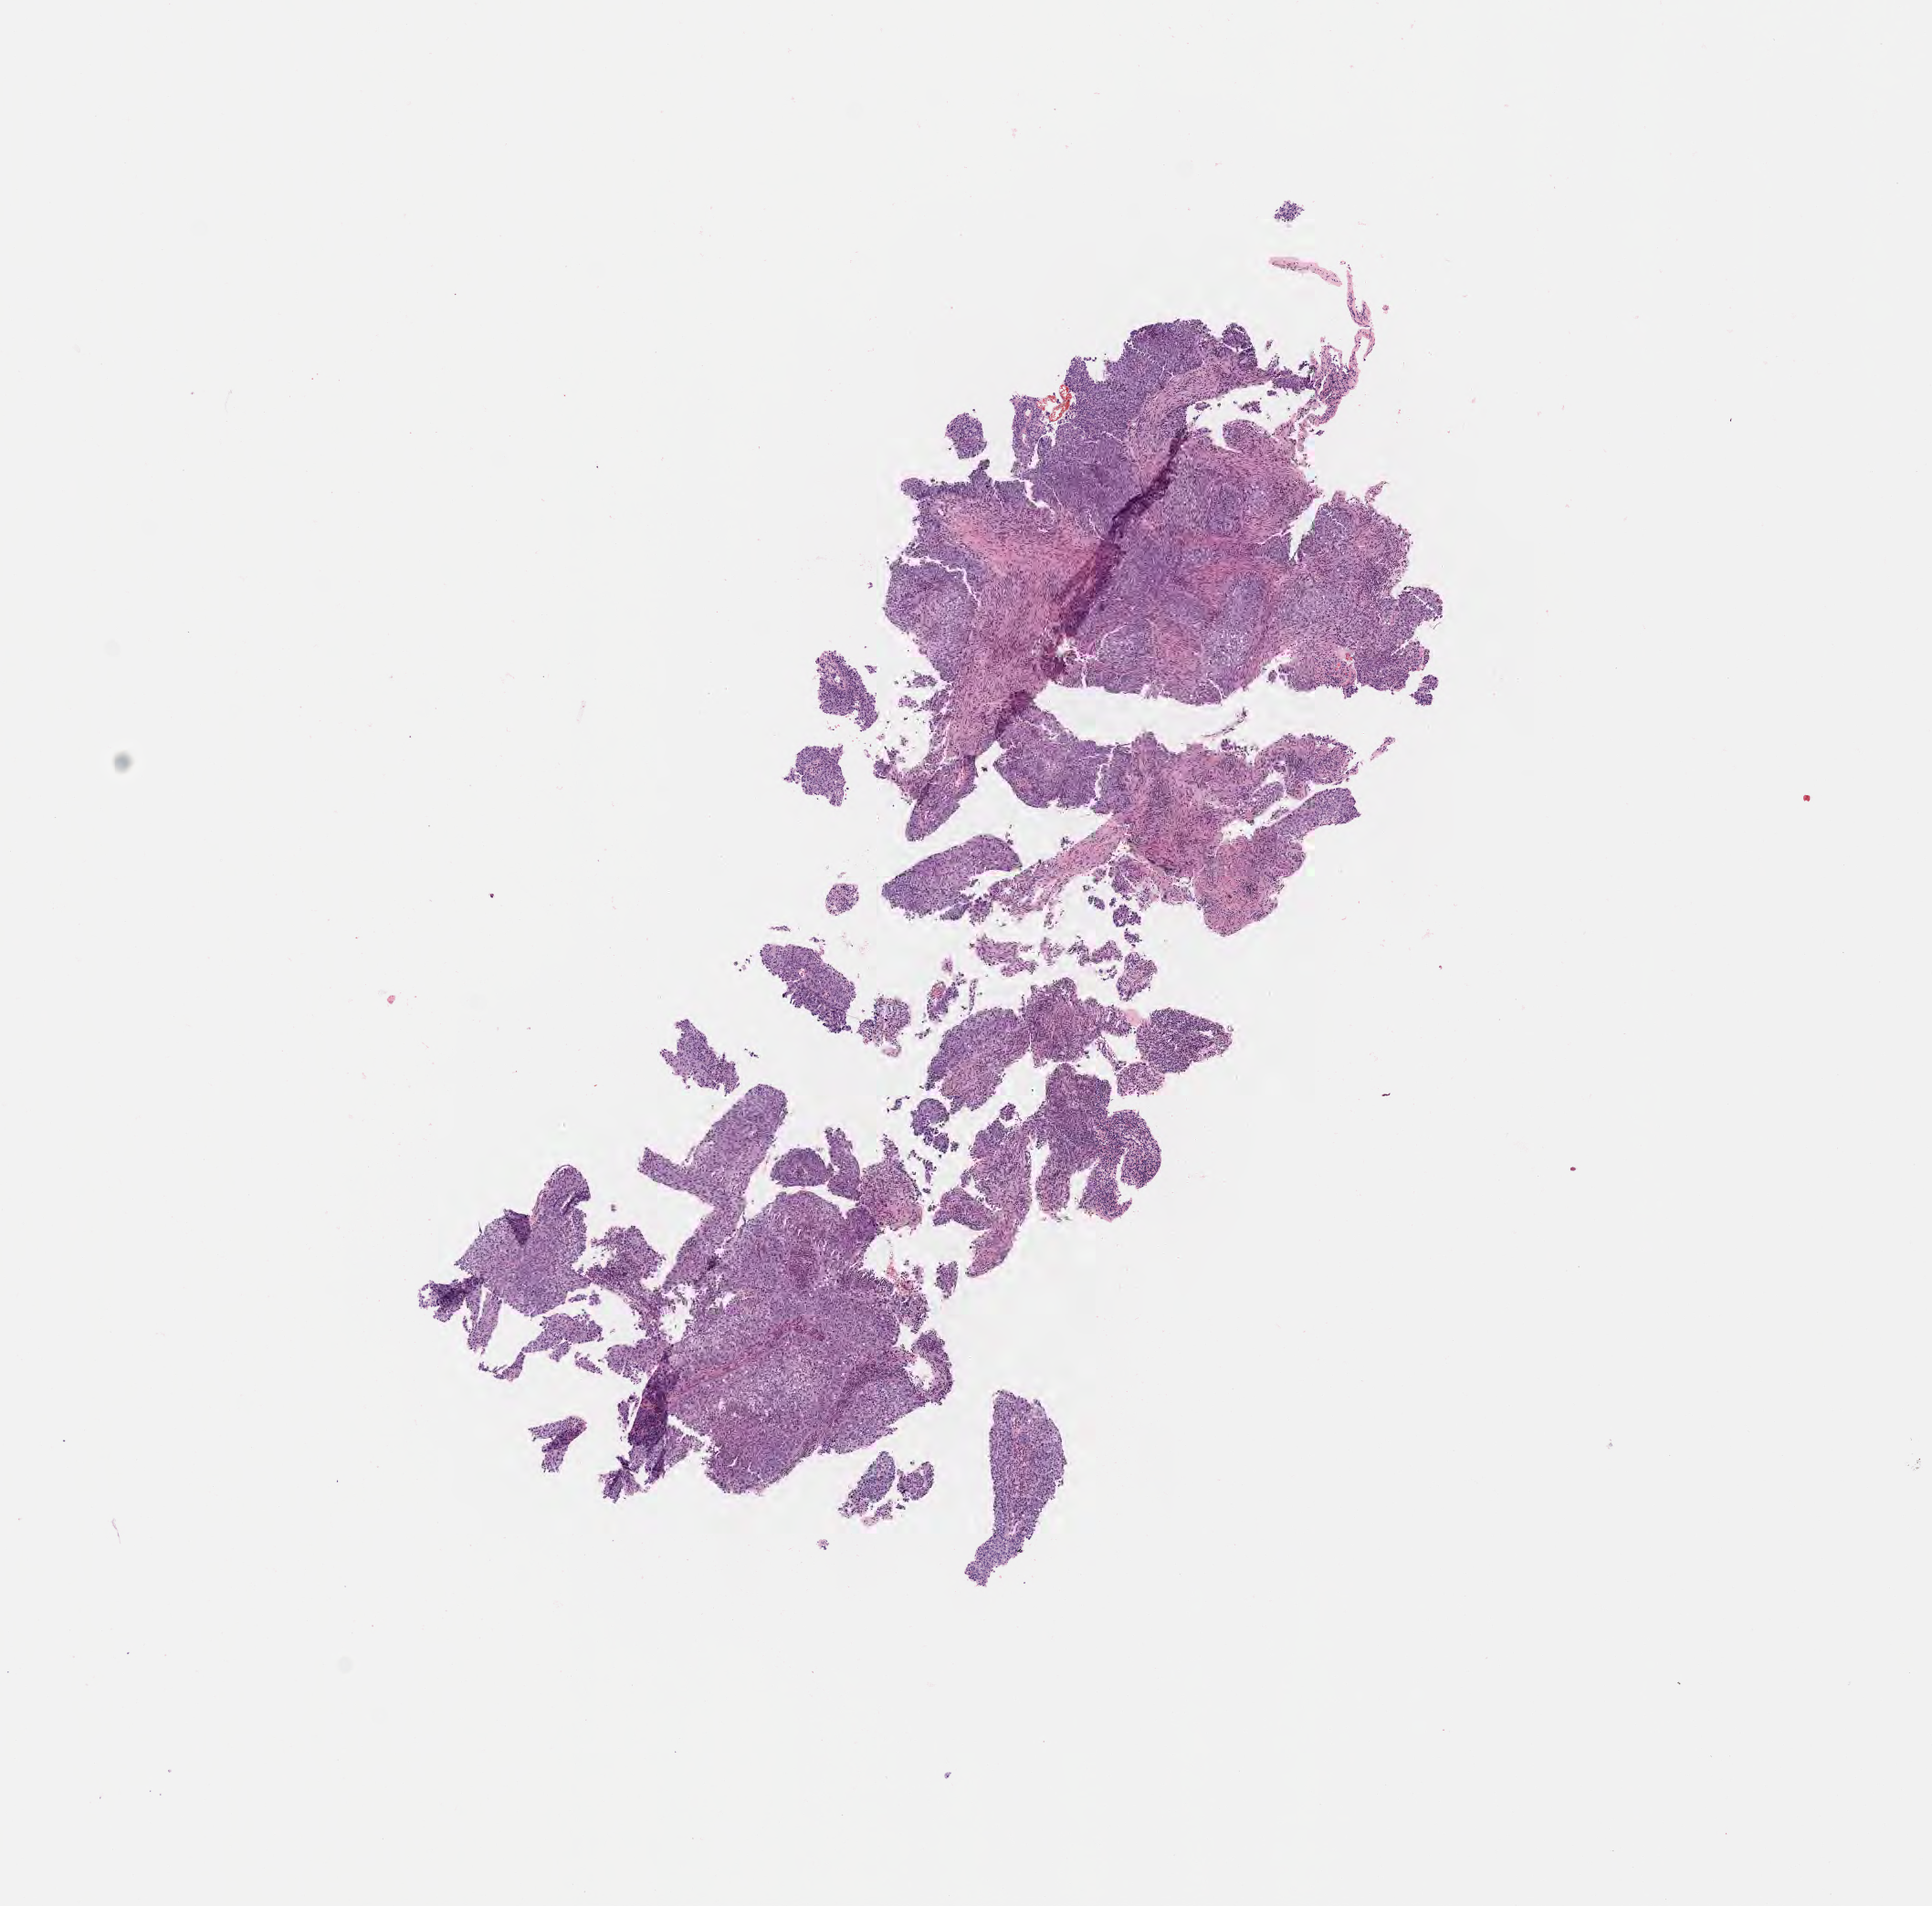
Hematoxylin and eosin (H&E) whole-slide image, whole scanned area (about 8.6 x 8.4 mm) shown as a low-resolution overview; specimen: tumor tissue; site: cervix. Patient: female, aged 31.
Diagnosis: Squamous cell carcinoma, large cell, nonkeratinizing, NOS.